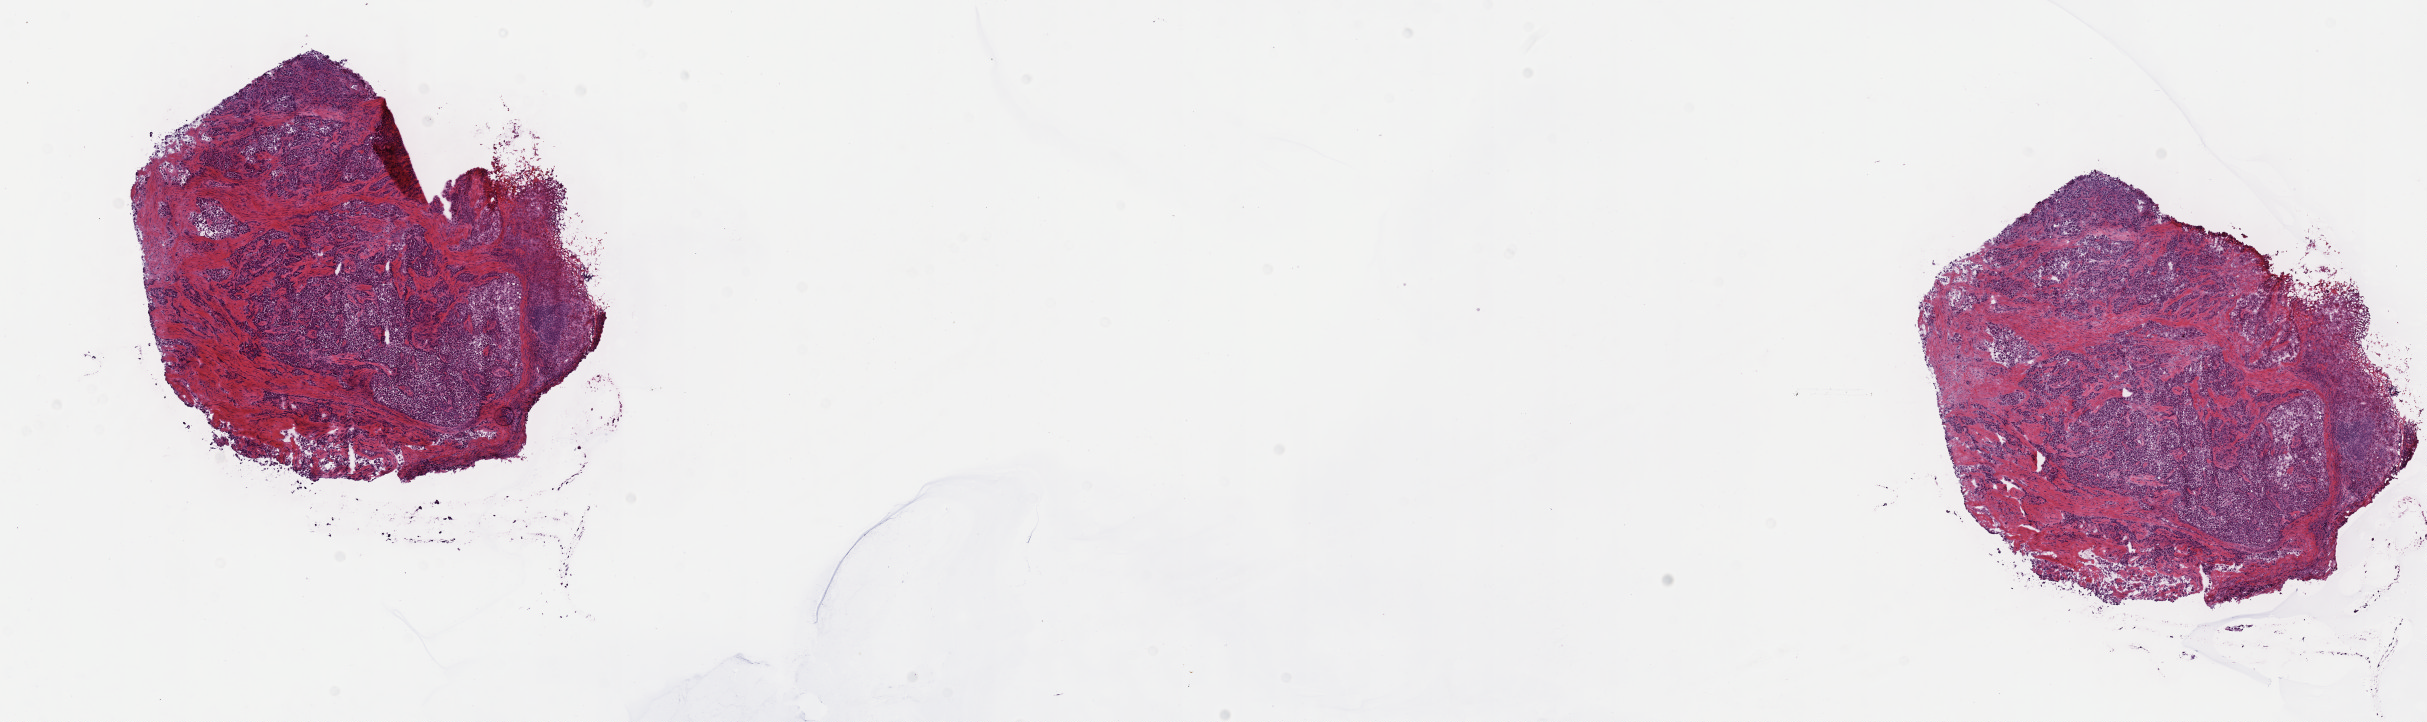
Digitized H&E-stained tissue section (whole slide) — shown as a low-resolution overview of the whole scanned area (about 19.6 x 5.8 mm); frozen section from the top of the tissue portion; sample: primary tumour, mesothelium. Male patient; age at initial diagnosis 60 years. Pathologist review of this section (percent, as recorded): tumour cells 70%, tumour nuclei 70%, normal cells 0%, stromal cells 30%, necrosis 0%. Infiltration values recorded for this section: lymphocyte infiltration 40%, monocyte infiltration 20%, neutrophil infiltration 20%.
- laterality: left
- AJCC pathologic stage: III (6th edition)
- diagnosis: Epithelioid mesothelioma, malignant (pleura, NOS)